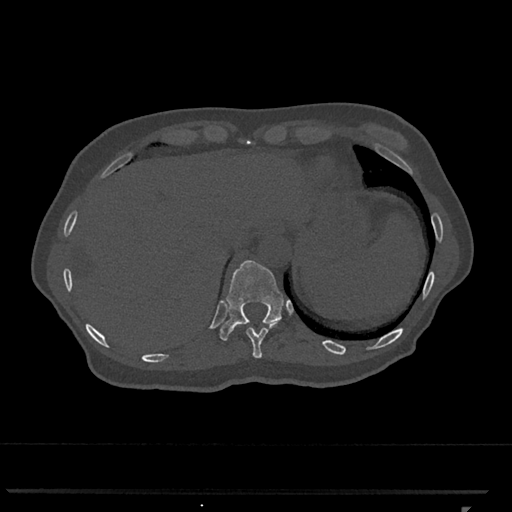
CT including the spine, one axial slice; slice 539 of 793 in the series (ordered by position); reconstruction kernel Br40s/3; 120 kVp; bone window (W 1800 / L 400 HU); 0.5 mm slice thickness; 512 × 512 image matrix. Patient: female, 62 years. Case-level facts recorded for this patient, not image findings: primary cancer: renal.
Structures marked on this image (semi-automatic segmentation, software-assisted and operator-edited):
- T10 vertebra: bounding box <237,322,278,358> (left, top, right, bottom; pixels)
- T11 vertebra: <219,260,284,341>